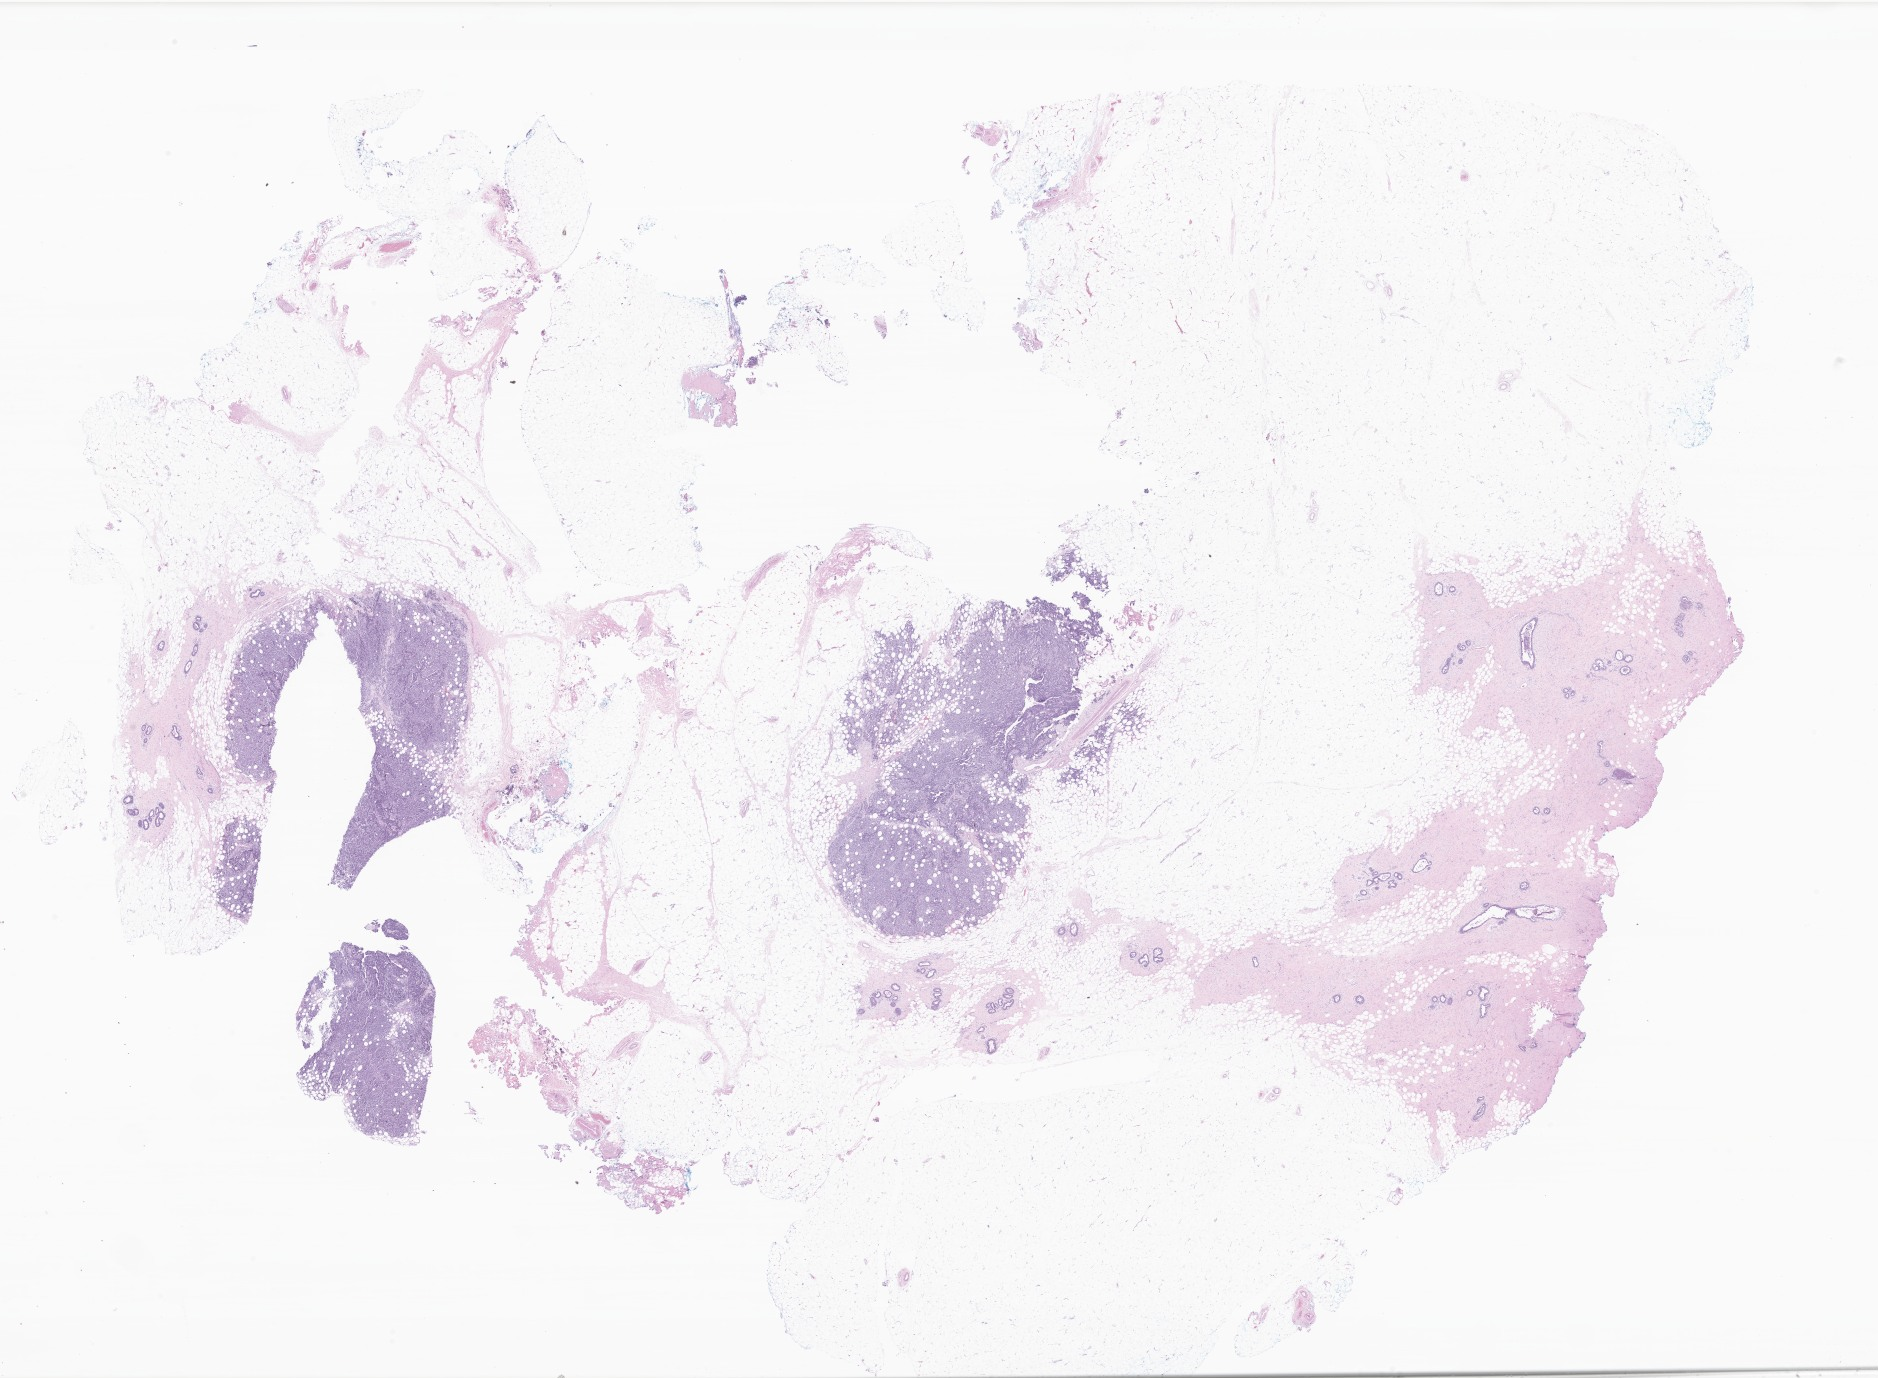
Haematoxylin and eosin whole-slide image of tumor tissue from the soft tissue of lower extremity — a low-resolution overview of the entire scanned area, about 31.7 x 23.2 mm, formalin-fixed paraffin-embedded section. Female patient, age 189 months (15 years 9 months).
Diagnosis: Rhabdomyosarcoma, NOS.